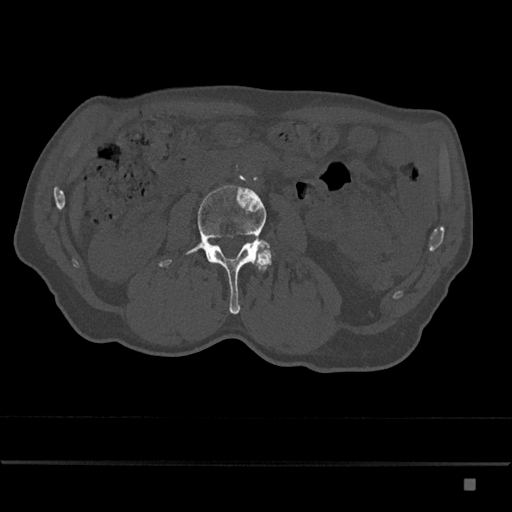
CT including the spine, one axial slice. Position 403 of 797 along the scan axis. Reconstruction kernel Br40s/3. 120 kVp. Bone window (W 1800 / L 400 HU). 512 × 512 image matrix, field of view 390 × 390 mm. Patient: male, 72 years. Case-level facts recorded for this patient, not image findings: primary cancer: prostate.
Annotated regions visible in this slice (semi-automatic segmentation, software-assisted and operator-edited):
- L3 vertebra: box from (x=158, y=185) to (x=270, y=314) px
- L4 vertebra: (x=256, y=248)–(x=272, y=271)